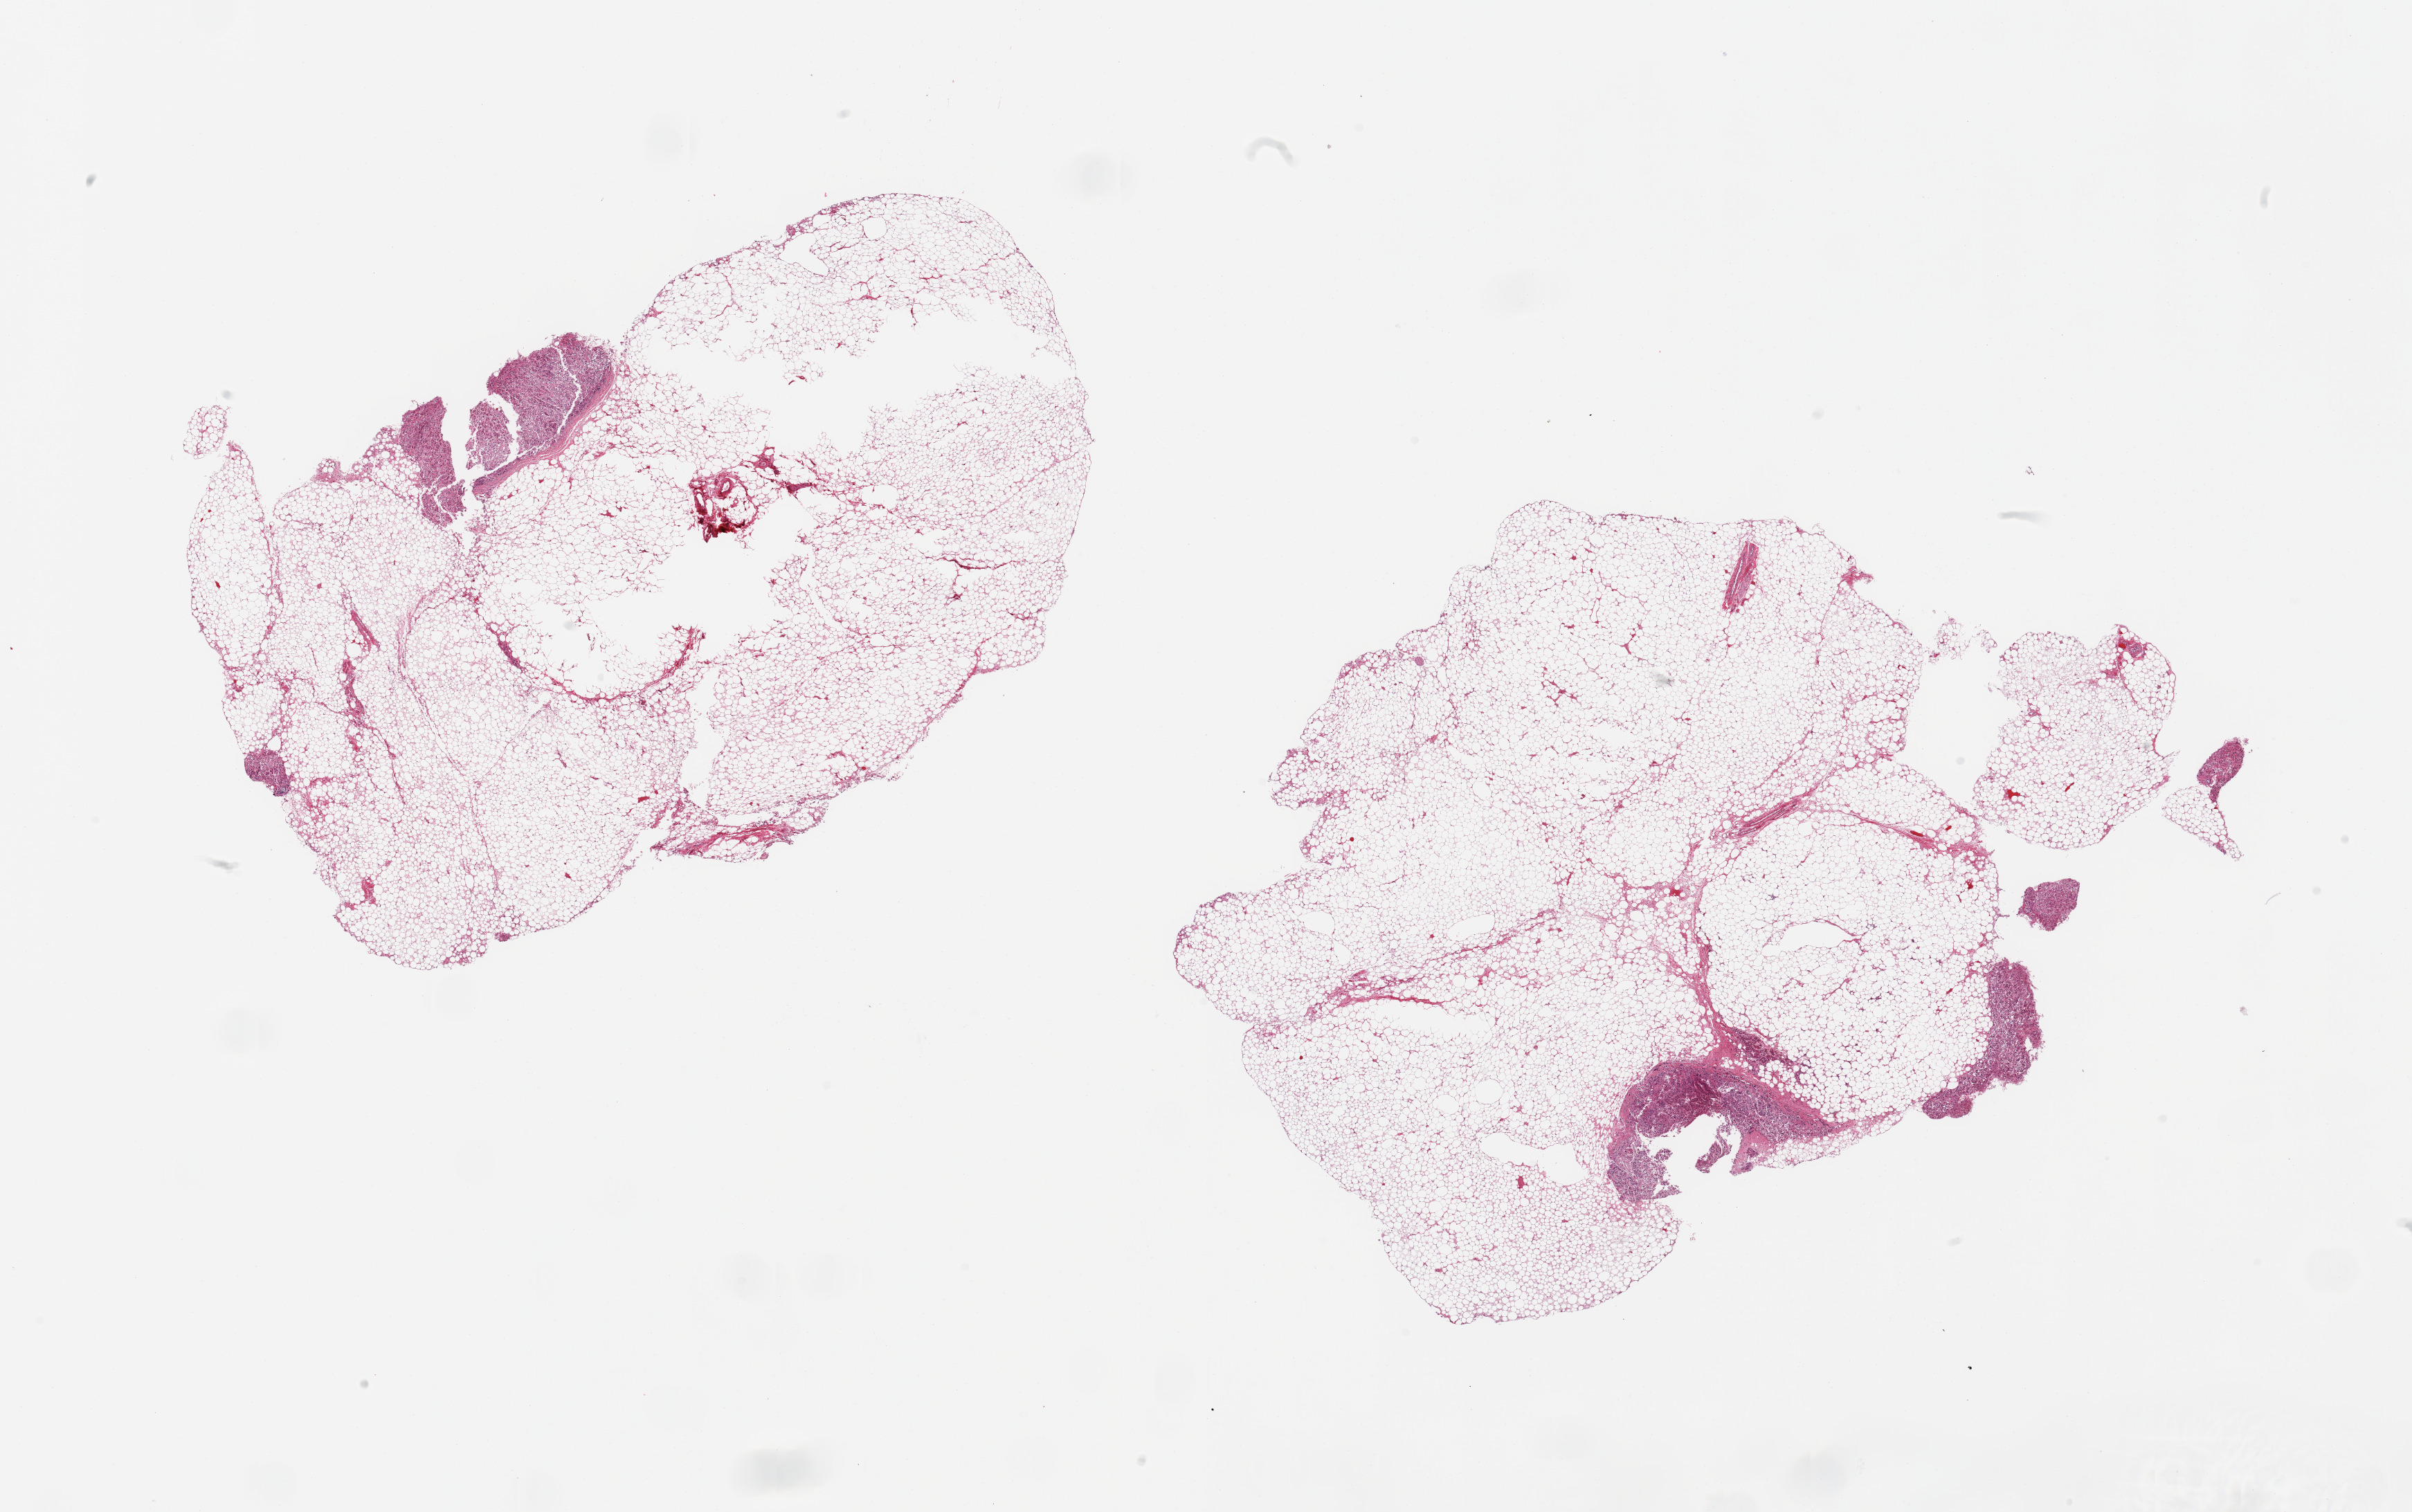
Hematoxylin and eosin (H&E) whole-slide image — low-resolution overview of the scanned area, about 27.6 x 17.3 mm (from a 20x scan); PAXgene-fixed, paraffin-embedded tissue; target tissue: adrenal gland; tissue donor sample. Donor sex: male.
Pathologist's review note for this sample: 2 pieces, ~90% fat, 10% autolyzed cortex.